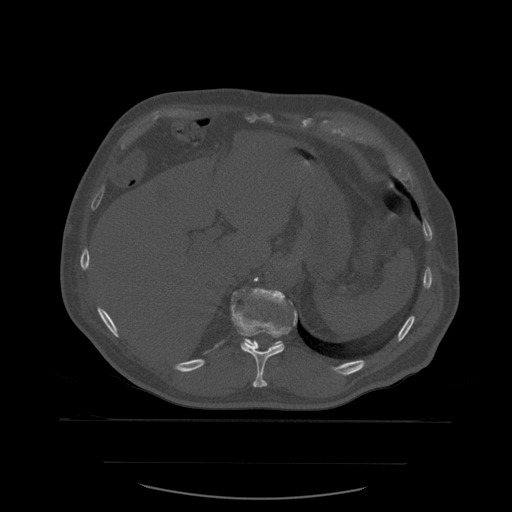
CT including the spine, one axial slice. Slice 290 of 590 in the series (ordered by position). Bone window (W 1800 / L 400 HU). 512 × 512 image matrix, field of view 479 × 479 mm. Patient age 71 years. Case-level facts recorded for this patient, not image findings: primary cancer: lung; vertebrae with lytic lesions (as recorded): T1, T2, L5, S1.
Structures marked on this image (semi-automatic segmentation, software-assisted and operator-edited):
- T11 vertebra: bounding box [x1, y1, x2, y2] px = [231, 290, 298, 388]
- T12 vertebra: [231, 288, 298, 346]